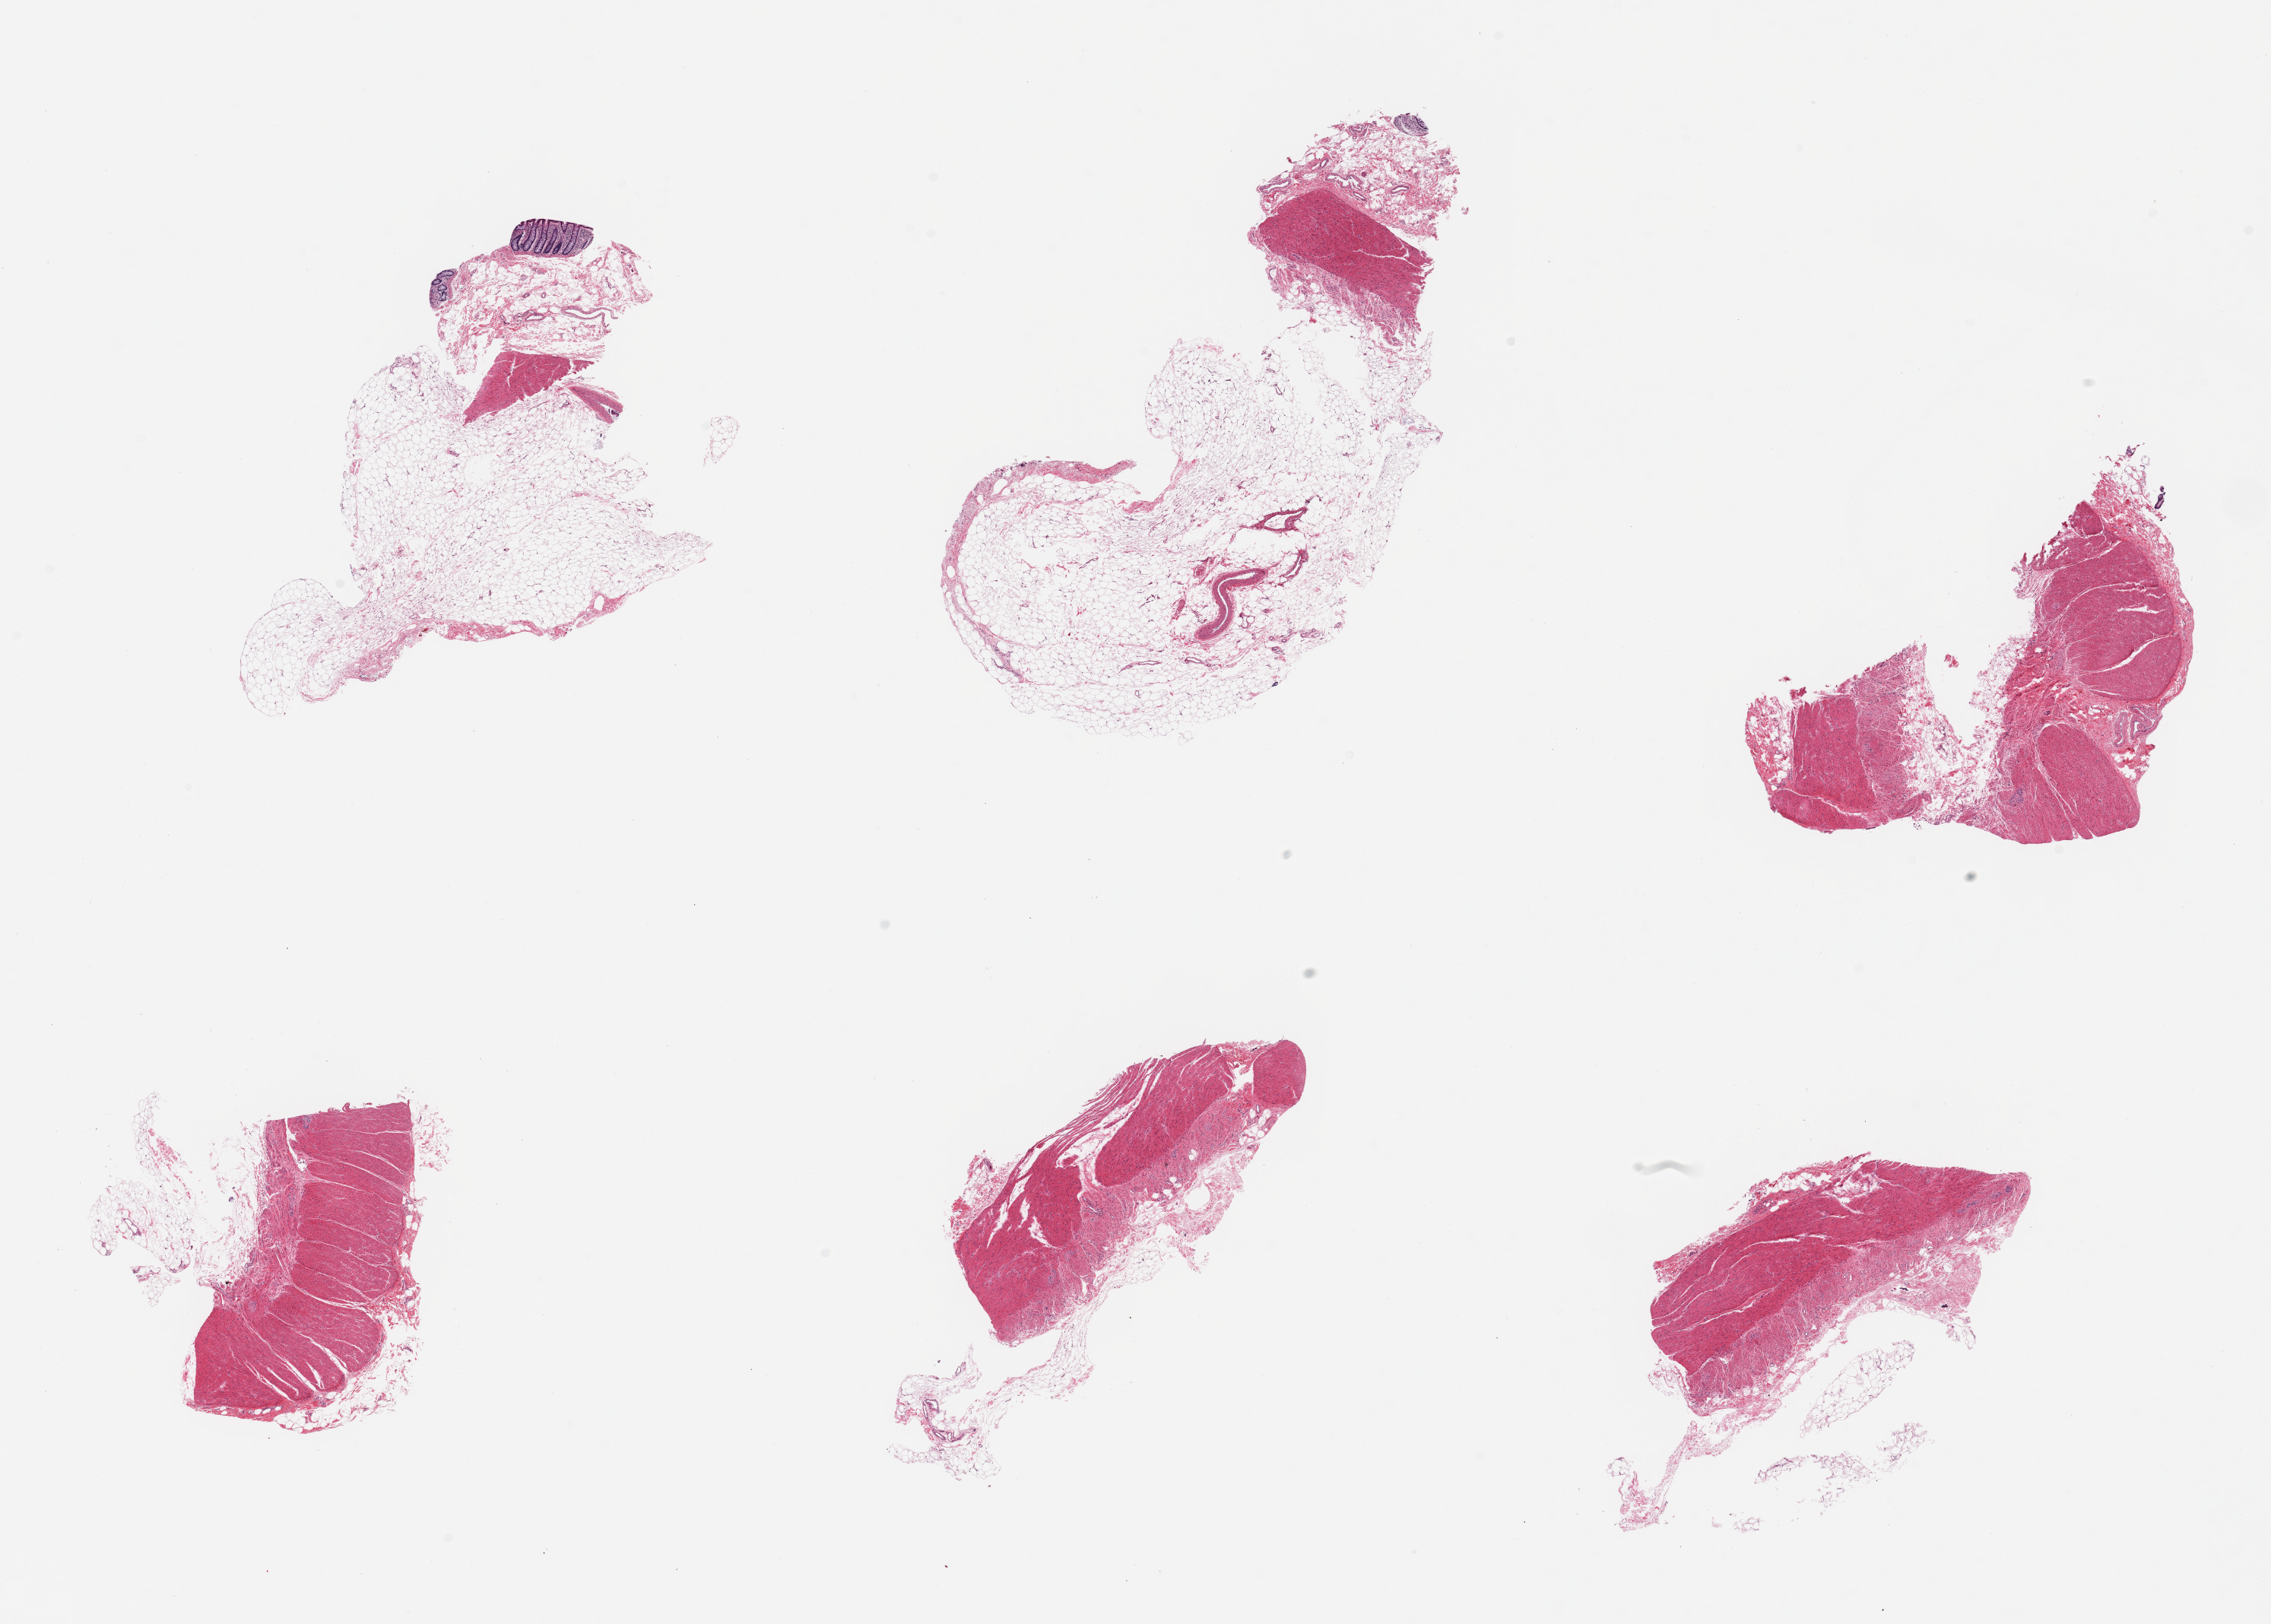
Digitized hematoxylin and eosin (H&E)-stained section — whole scanned area (about 23.6 x 16.9 mm, slide scanned at 20x) shown as a low-resolution overview. PAXgene-fixed paraffin-embedded (PFPE) section. Sampled site (target tissue): transverse colon. Tissue donor sample. Donor: male.
Reviewer comment on this tissue sample: 6 pieces; muscularis and fat without significant amount of mucosa.